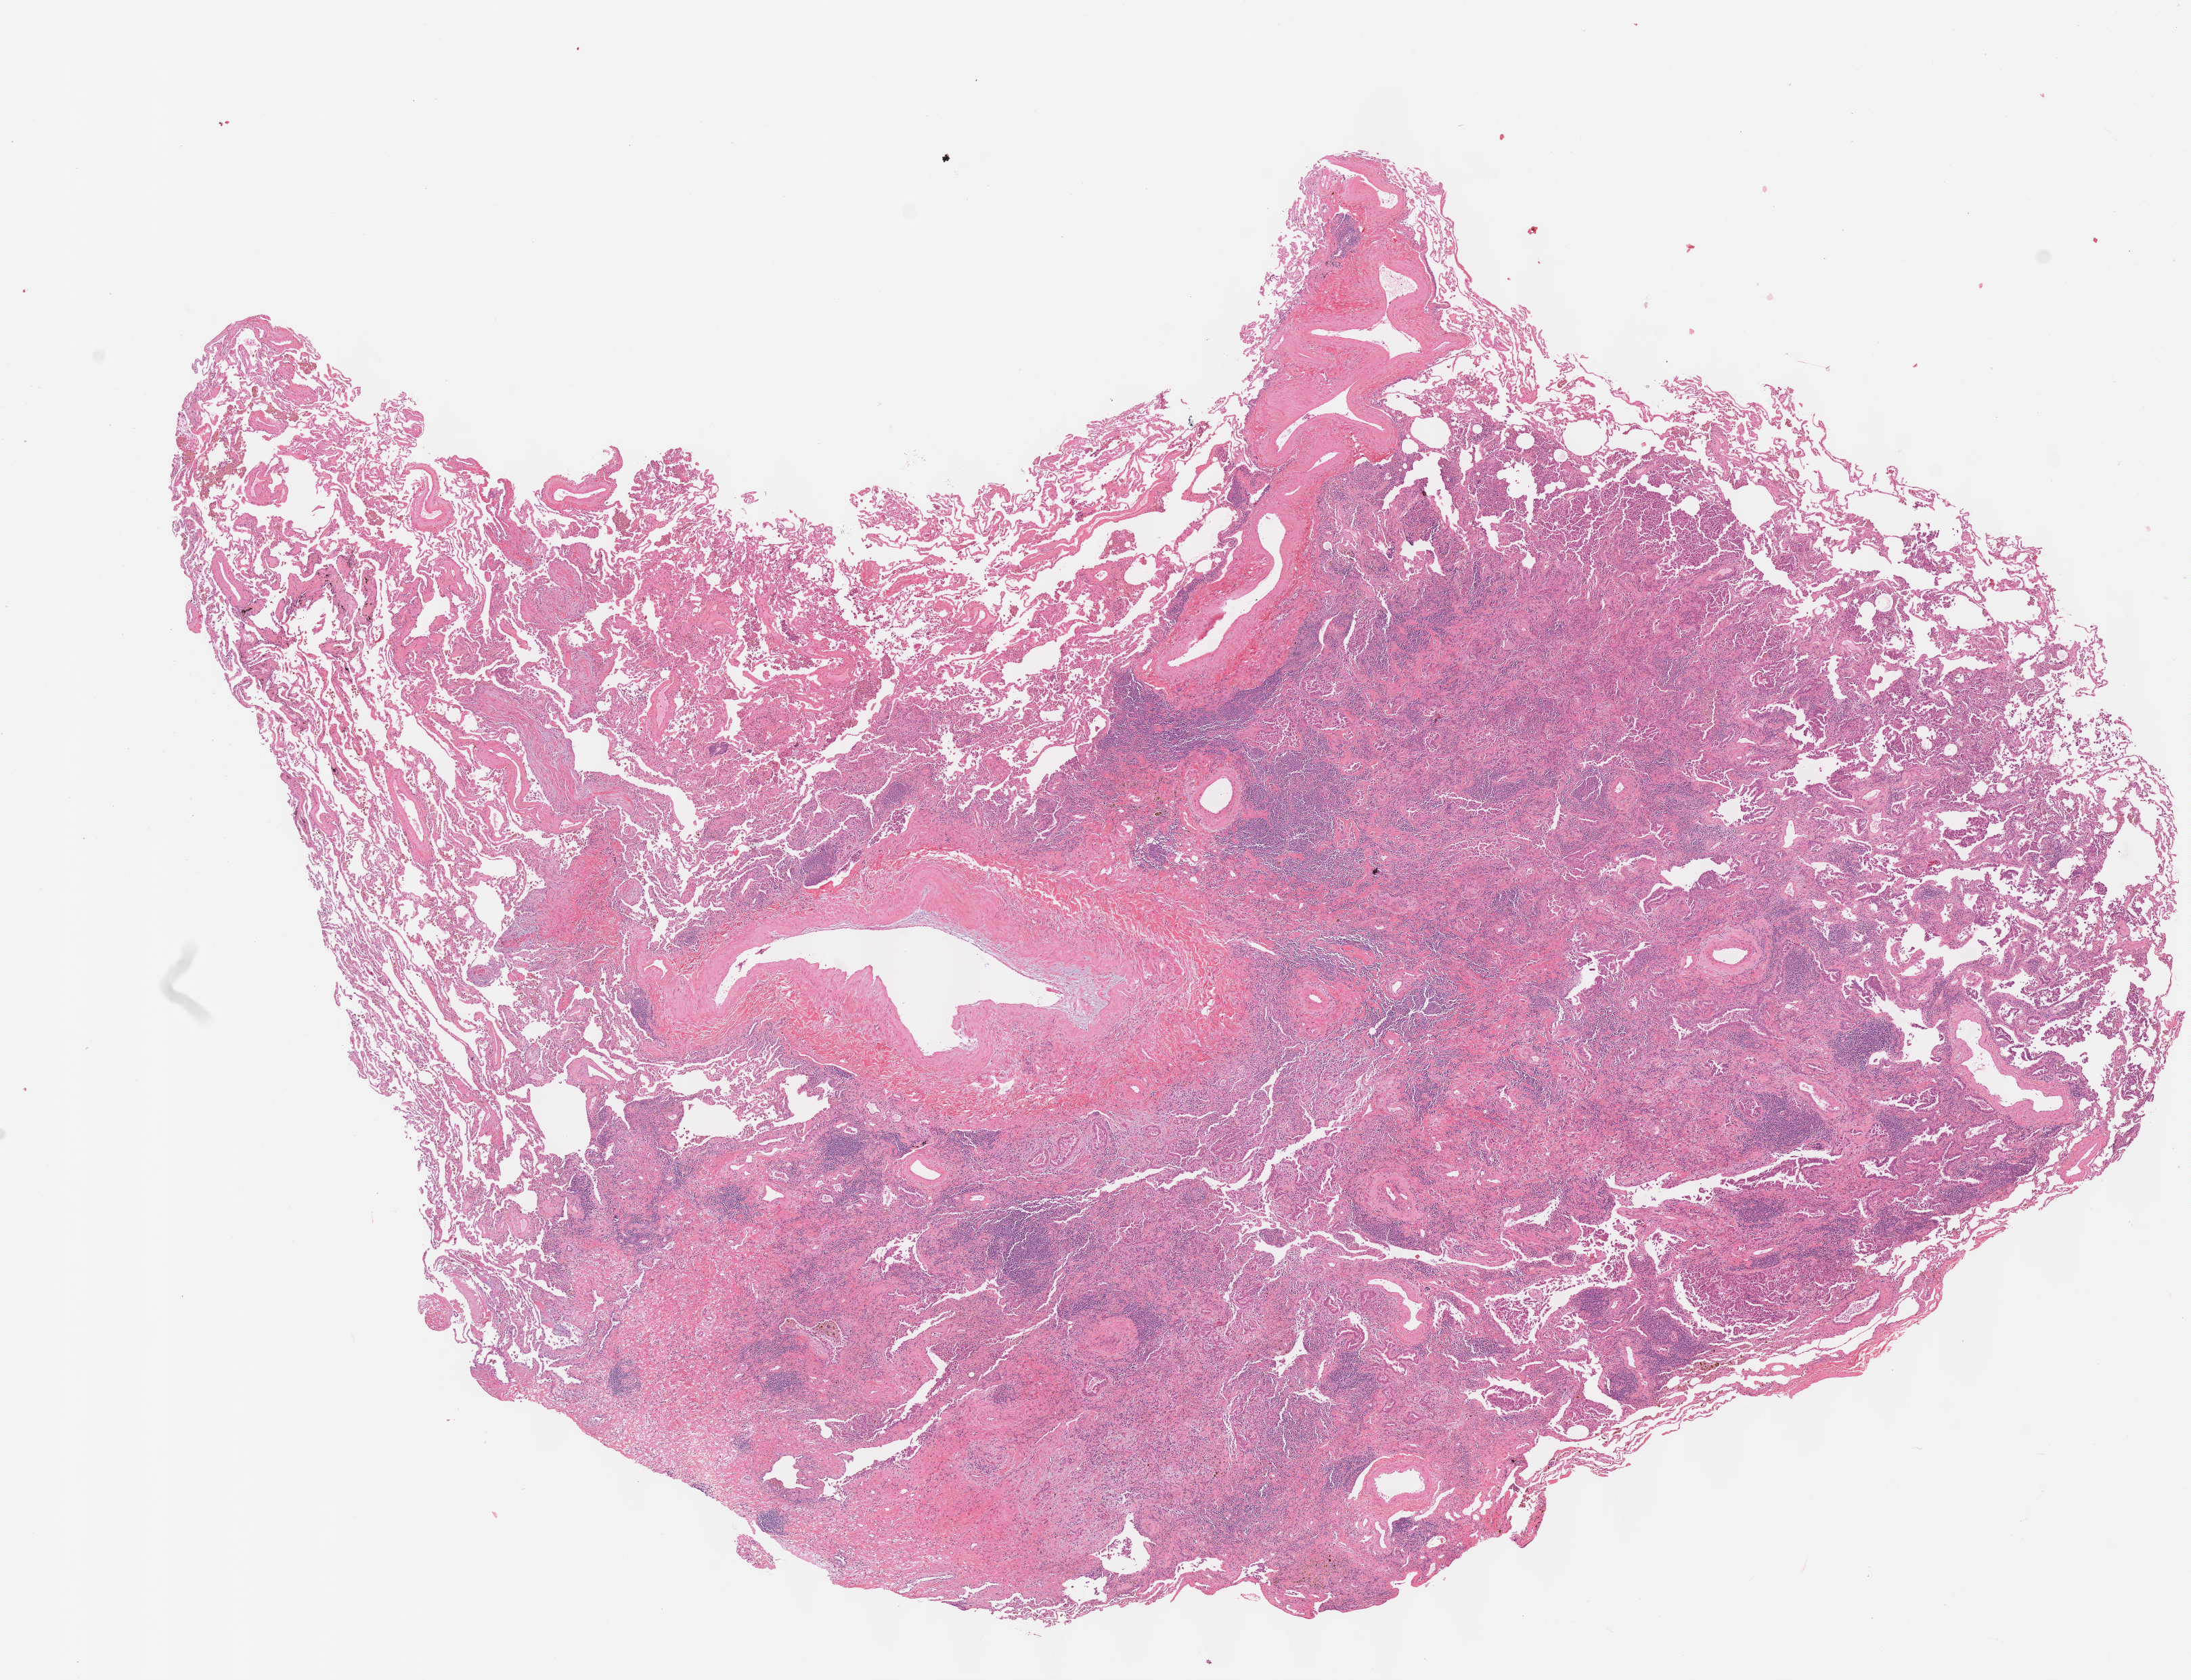
H&E whole-slide image — a low-resolution overview of the entire scanned area, about 13.1 x 10.0 mm (slide scanned at 40x); formalin-fixed paraffin-embedded (FFPE) diagnostic section; sample: primary tumour, lung. Patient: female, age at initial diagnosis 70 years.
Diagnosis: Adenocarcinoma, NOS.